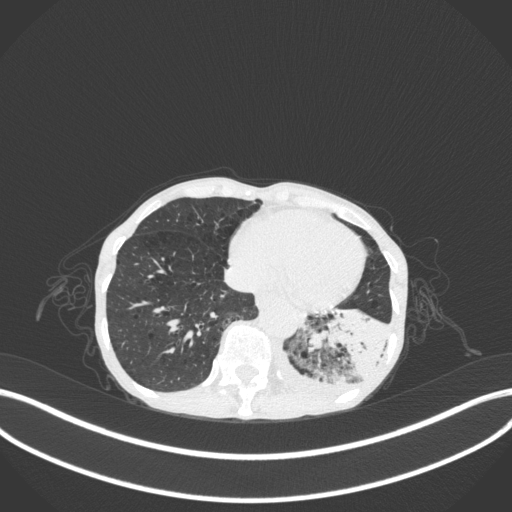
Chest CT, one axial slice; slice 56 of 347 in the series (ordered by position); reconstruction kernel B31f; 120 kVp; lung window (W 1500 / L -600 HU); 512 × 512 image matrix. Patient: female, 70 years. From the clinical record (not read from this slice): clinical TNM (as recorded): T3 N0 M0; histopathological grade: G3.
Structures marked on this image (rectangle marked by the reading radiologist):
- lung tumour (recorded histology: small cell carcinoma): bounding box (x1, y1, x2, y2) in pixels: (305, 296, 392, 392)